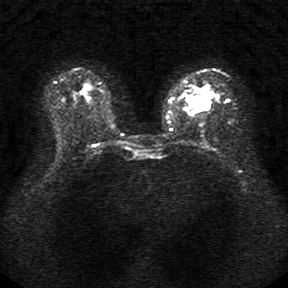
Breast MRI, one axial slice. Slice 17 of 34 in the series (ordered by position). Diffusion-weighted series; image 2 of 4 stored at this slice position (different b-values; order by instance number). 1.5 T. 5 mm slice thickness. 288 × 288 image matrix, field of view 340 × 340 mm. Female patient.
Structures marked on this image (outlined manually by an expert reader):
- tumour on diffusion-weighted imaging: bounding box <193,97,205,110> (left, top, right, bottom; pixels)